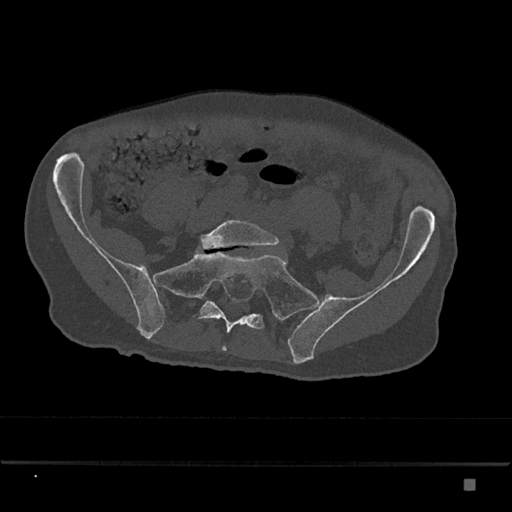
CT including the spine, one axial slice; bone window (W 1800 / L 400 HU); 0.5 mm slice thickness; 512 × 512 image matrix, field of view 390 × 390 mm. Patient: male, 72 years. From the clinical record (not read from this slice): primary cancer: prostate.
Annotated regions visible in this slice (semi-automatically segmented with operator editing):
- L5 vertebra: box from (x=200, y=220) to (x=280, y=249) px